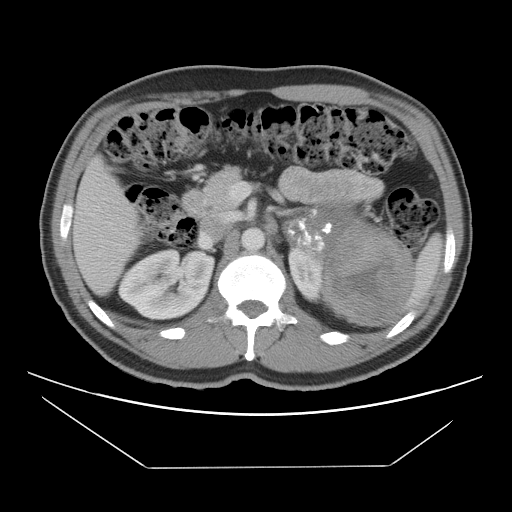
Contrast-enhanced abdominal CT, one axial slice. Position 67 of 131 along the scan axis. Reconstruction kernel STANDARD. Soft-tissue window (W 400 / L 40 HU). 512 × 512 image matrix, field of view 396 × 396 mm. Male patient, age 44 years. Case-level facts recorded for this patient, not image findings: diagnosis: adrenocortical carcinoma; tumour side: left adrenal.
Outlined on this slice (semi-automatically segmented with operator editing):
- mass: box from (x=285, y=210) to (x=412, y=322) px